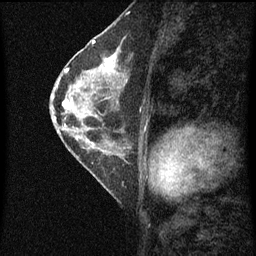
Breast MRI (dynamic contrast-enhanced), one sagittal slice. Position 36 of 60 along the scan axis. Dynamic contrast-enhanced series, image 2 of 4 at this slice position (ordered by acquisition). 1.5 T. TE 4.2 ms, TR 8 ms. 2 mm slice thickness. 256 × 256 image matrix. Female patient, age 56 years.
Outlined on this slice (semi-automatically segmented with operator editing):
- analysis volume of interest (the breast-tissue region the enhancement analysis was run in; not a lesion): box from (x=56, y=52) to (x=129, y=115) px
- tumour enhancement mask (voxels above the 70 % enhancement threshold inside the analysis volume of interest): (x=56, y=56)–(x=117, y=109)